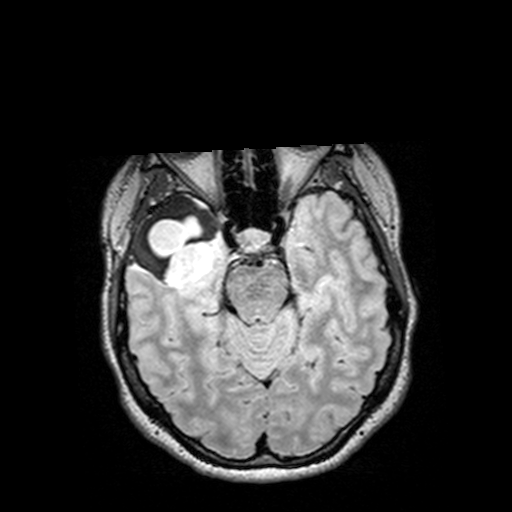
Brain MRI from a brain-tumour surgery series, one axial slice; slice 94 of 144 in the series (ordered by position); T2 FLAIR; 512 × 512 image matrix, field of view 250 × 250 mm. Case-level facts recorded for this patient, not image findings: histopathology: Astrocytoma; WHO grade: 3.
Structures marked on this image (outlined manually by an expert reader):
- tumour: bounding box <126,193,232,287> (left, top, right, bottom; pixels)